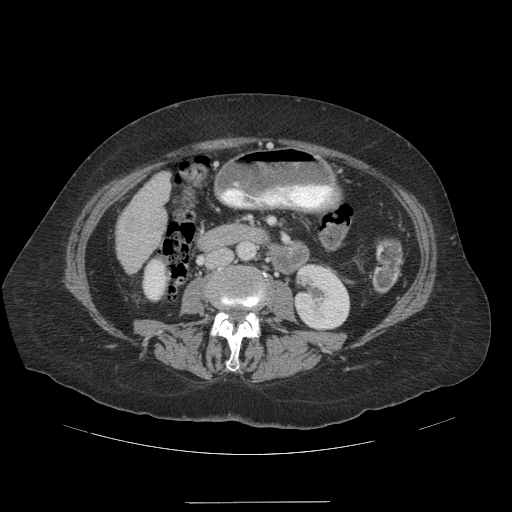
Contrast-enhanced abdominal CT (liver protocol), one axial slice. Slice 35 of 99 in the series (ordered by position). Reconstruction kernel STANDARD. 140 kVp. Soft-tissue window (W 400 / L 40 HU). 512 × 512 image matrix, field of view 440 × 440 mm. Case-level facts recorded for this patient, not image findings: diagnosis: hepatocellular carcinoma (patient treated with transarterial chemoembolisation; whether this scan precedes or follows treatment is not stated here); TNM stage (as recorded): Stage-IVA; Child-Pugh class: A; tumour nodularity: multinodular.
Outlined on this slice (semi-automatically segmented with operator editing):
- liver parenchyma outside the tumour (the mass and vessels are separate outlines, so this box may not span the whole liver): box from (x=116, y=172) to (x=170, y=272) px